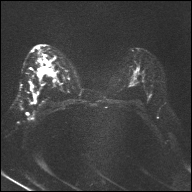
Breast MRI, one axial slice; slice 17 of 32 in the series (ordered by position); diffusion-weighted series; image 2 of 4 stored at this slice position (different b-values; order by instance number); 1.5 T; 4 mm slice thickness; 192 × 192 image matrix, field of view 360 × 360 mm. Female patient.
Outlined on this slice (outlined manually by an expert reader):
- tumour on diffusion-weighted imaging: bounding box (x1, y1, x2, y2) in pixels: (40, 60, 45, 71)